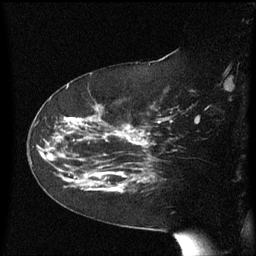
Breast MRI (dynamic contrast-enhanced), one sagittal slice; slice 37 of 60 in the series (ordered by position); dynamic contrast-enhanced series, image 2 of 3 at this slice position (ordered by acquisition); 1.5 T; TE 4.2 ms, TR 8.4 ms; 256 × 256 image matrix. Female patient, age 63 years. Case-level facts recorded for this patient, not image findings: setting: breast cancer imaged before/during neoadjuvant chemotherapy; receptor status: HER2-positive.
Annotated regions visible in this slice (semi-automatically segmented with operator editing):
- analysis volume of interest (the breast-tissue region the enhancement analysis was run in; not a lesion): bounding box [x1, y1, x2, y2] px = [63, 144, 147, 206]
- tumour enhancement mask (voxels above the 70 % enhancement threshold inside the analysis volume of interest): [91, 172, 145, 192]